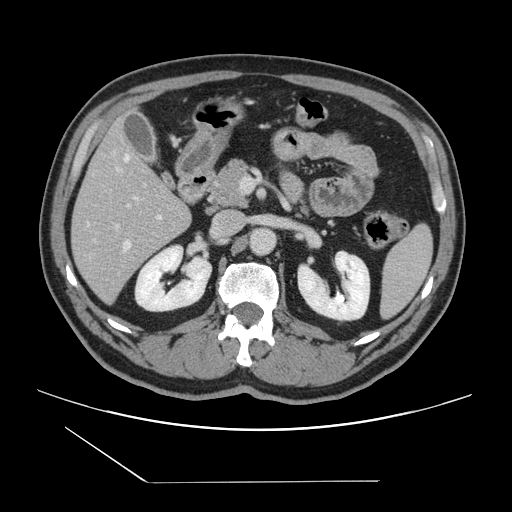
Contrast-enhanced abdominal CT, one axial slice; position 69 of 157 along the scan axis; 120 kVp; intravenous contrast given; soft-tissue window (W 400 / L 40 HU); 2.5 mm slice thickness; 512 × 512 image matrix, field of view 407 × 407 mm. Male patient, age 61 years. Case-level facts recorded for this patient, not image findings: diagnosis: colorectal cancer liver metastases, imaged before liver resection.
Outlined on this slice (manually delineated by an expert):
- hepatic veins: bounding box (x1, y1, x2, y2) in pixels: (123, 155, 138, 250)
- liver: (73, 127, 191, 302)
- planned liver remnant (the part of the liver to remain after resection): (74, 125, 178, 219)
- portal vein (with intrahepatic branches): (116, 168, 161, 227)